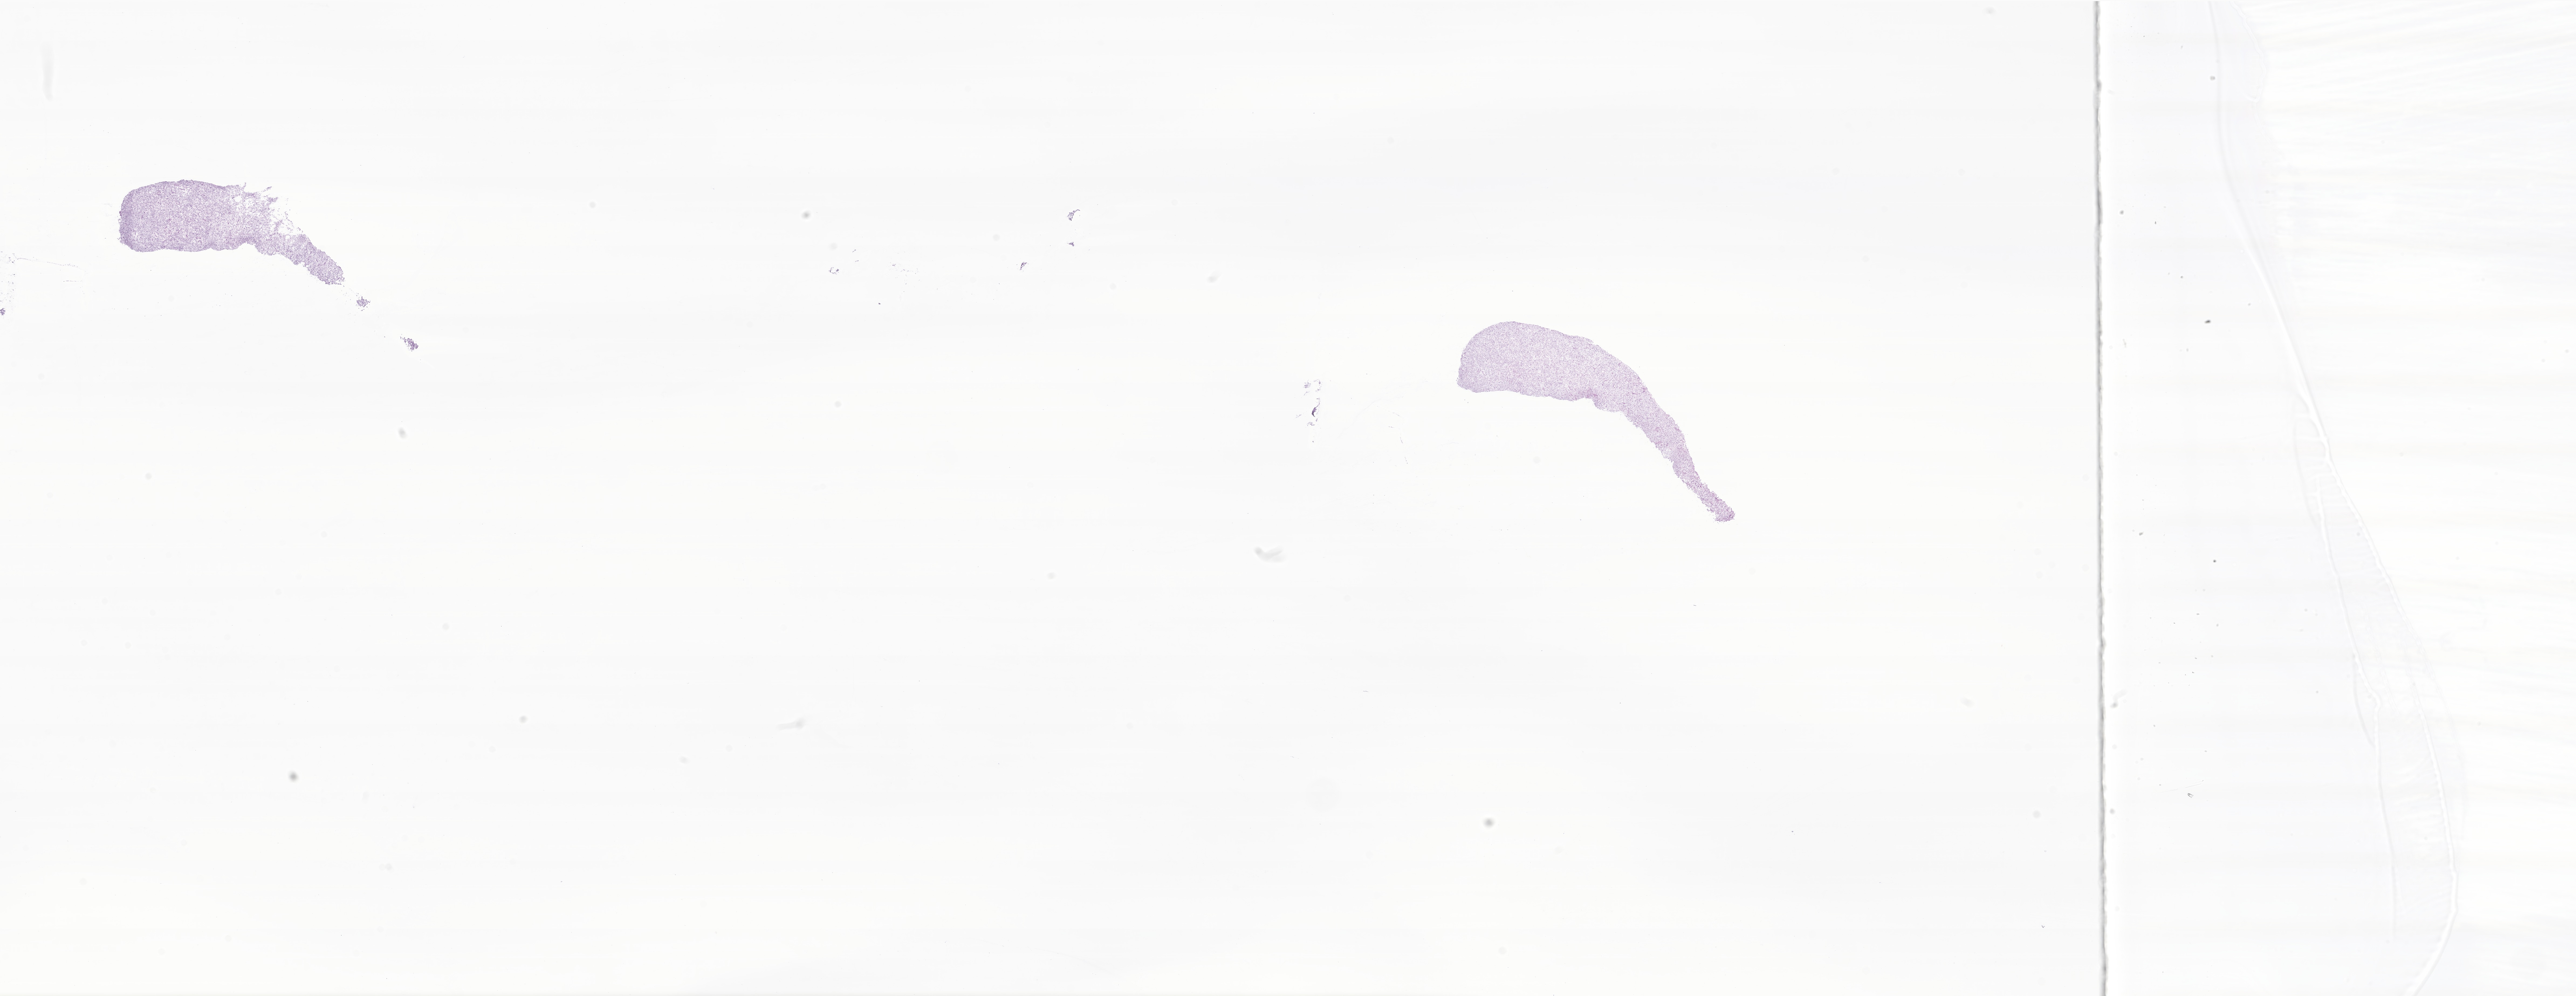
Whole-slide image, haematoxylin and eosin stain of tumor tissue from the lower limb, whole scanned area (about 40.3 x 15.6 mm) shown as a low-resolution overview; frozen section (OCT-embedded). Male patient, age 920 days (about 2.5 years).
• diagnosis: Dermatofibrosarcoma protuberans, fibrosarcomatous